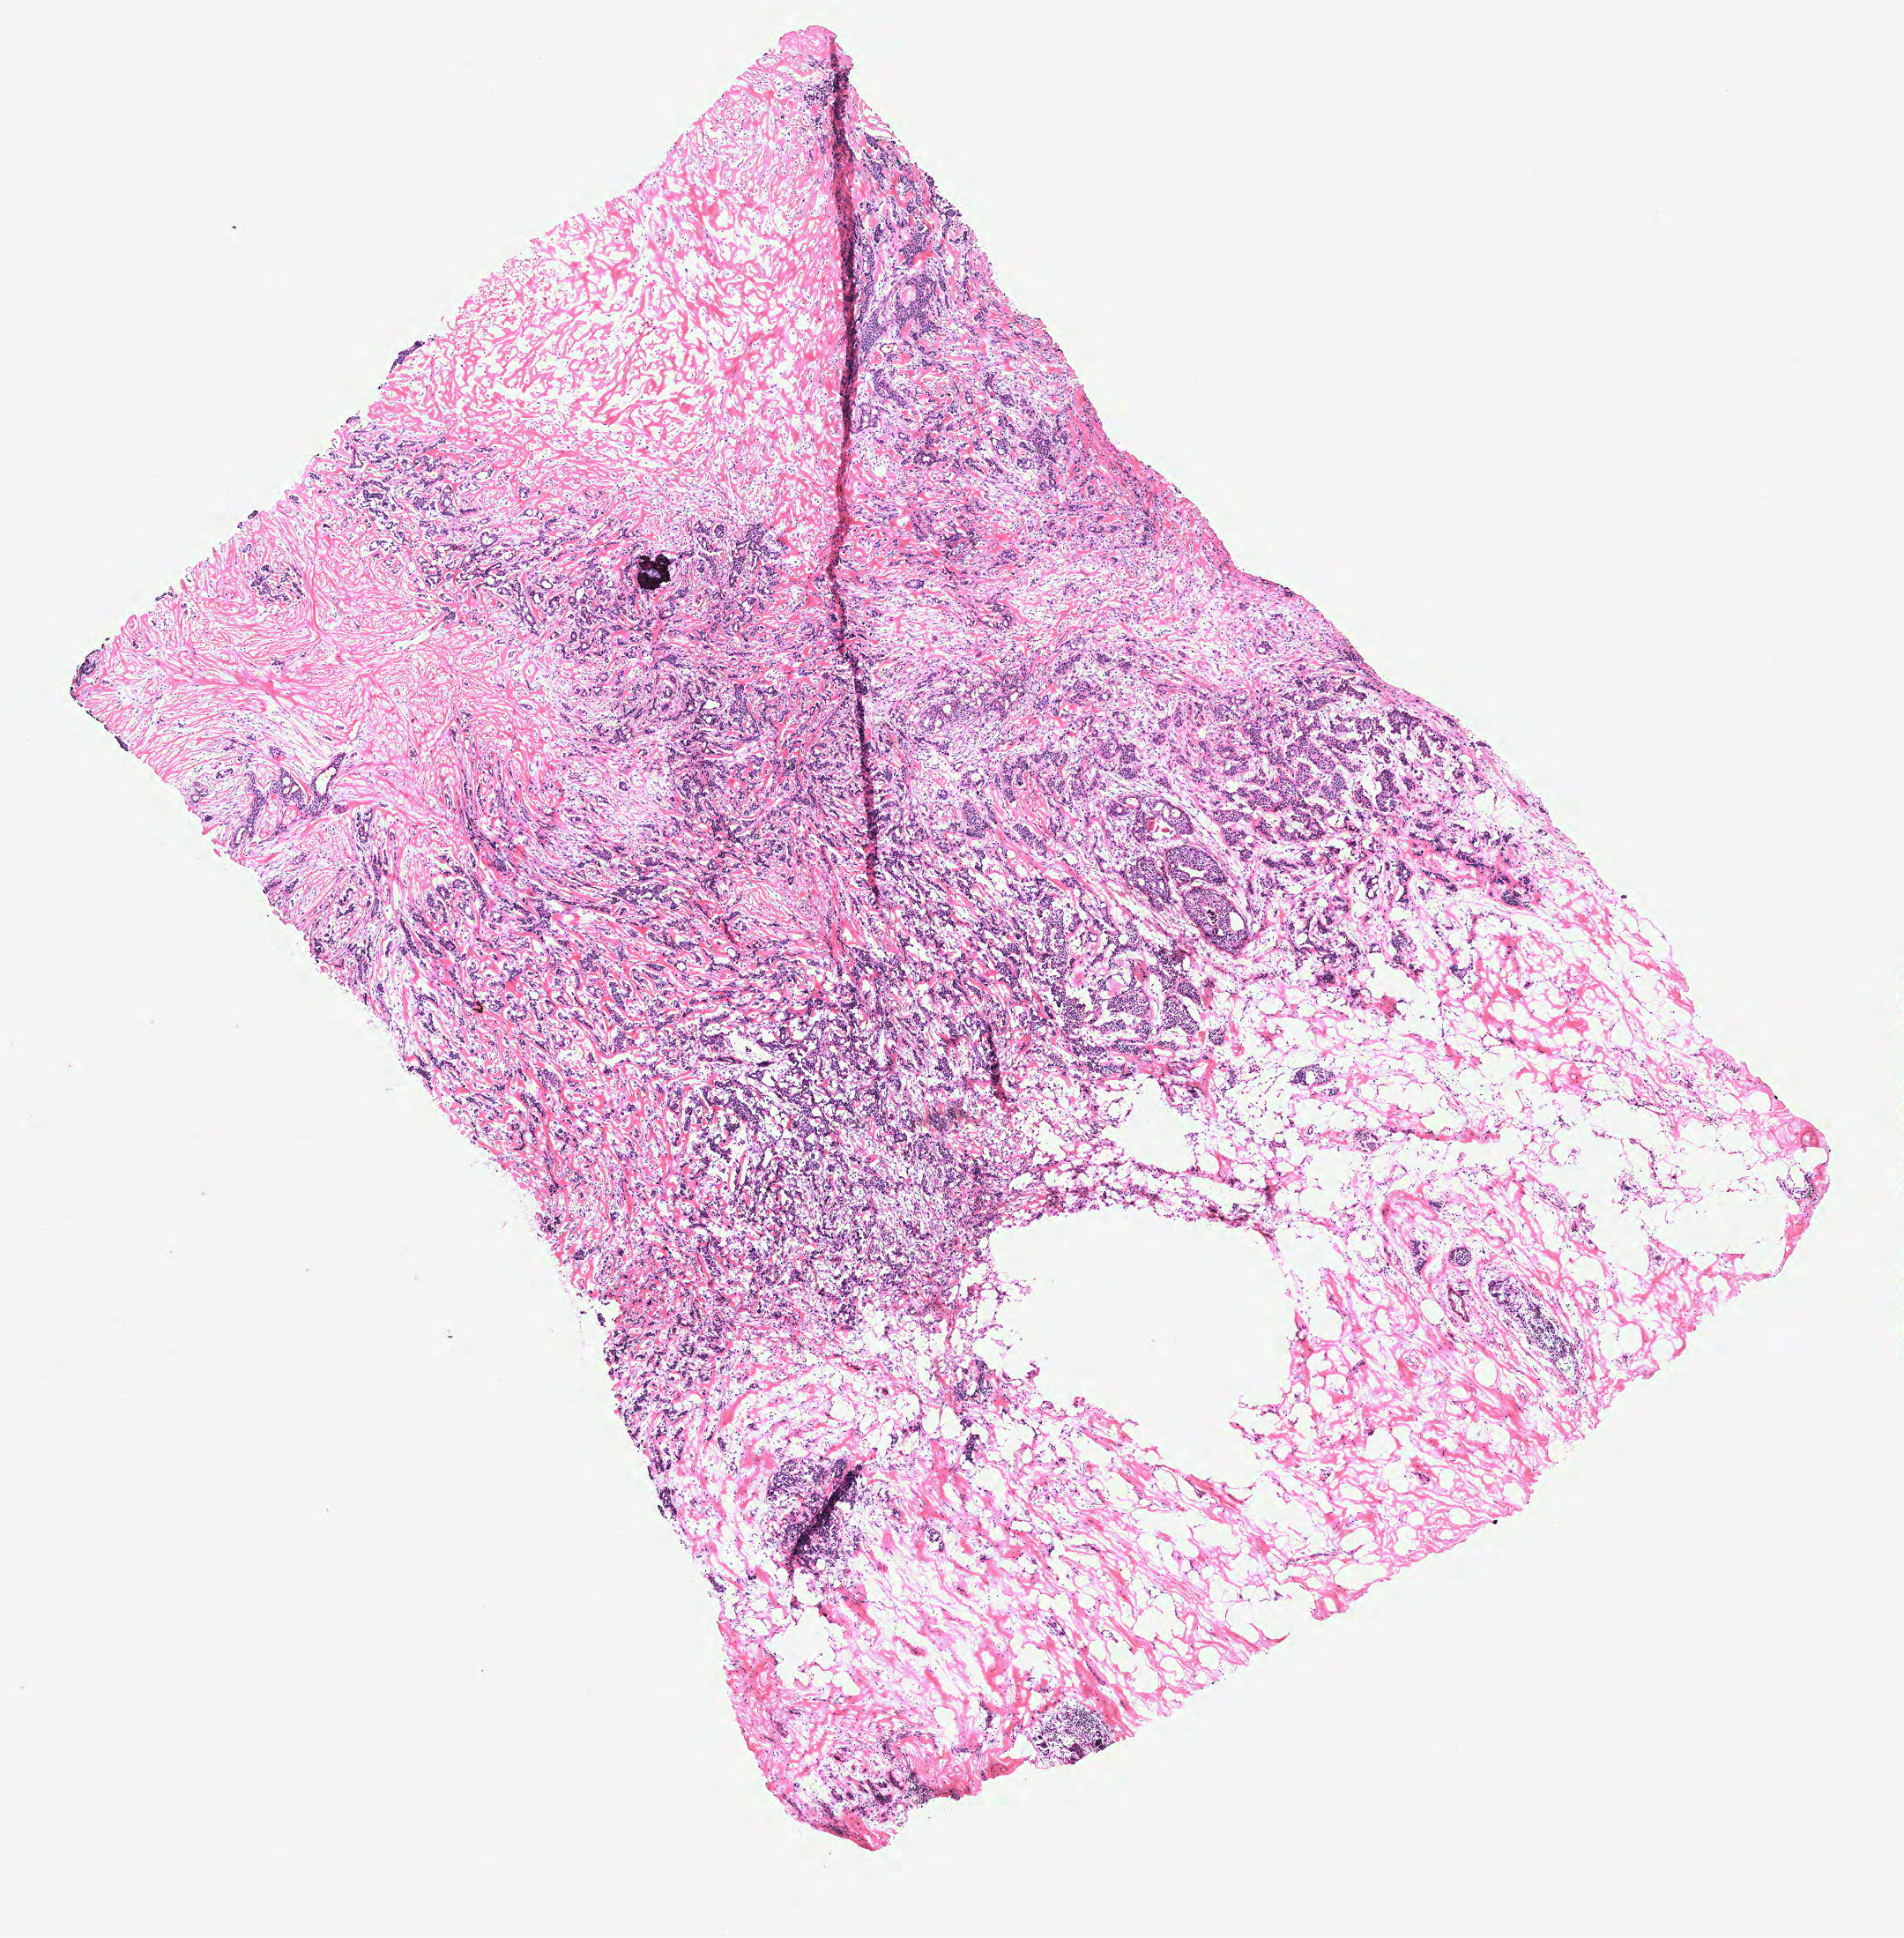
Hematoxylin and eosin (H&E) stained whole-slide image, shown as a low-resolution overview of the whole scanned area (about 8.6 x 8.8 mm, from a 40x scan). Breast, tissue type not recorded.
- patient diagnosis (cohort enrolment): breast cancer (breast)